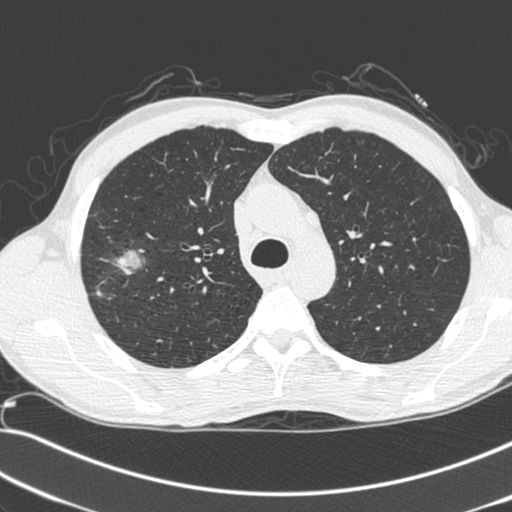
Low-dose screening chest CT, axial slice. Baseline annual screen. Lung window (W 1500 / L -600 HU). 1.3 mm slice thickness. Standard (soft-tissue) reconstruction kernel (C). 120 kVp. 512 × 512 image matrix. Male participant, aged 55 years at enrolment. Current smoker at enrolment.
Lesion marked by an expert reader, bounding box <73,238,150,309> (left, top, right, bottom; pixels). The exam's reader record, not a measurement of the box and not confirmed to be the same lesion: non-calcified nodule or mass ≥4 mm, right upper lobe, 52 × 39 mm, spiculated (stellate) margins, soft tissue attenuation.